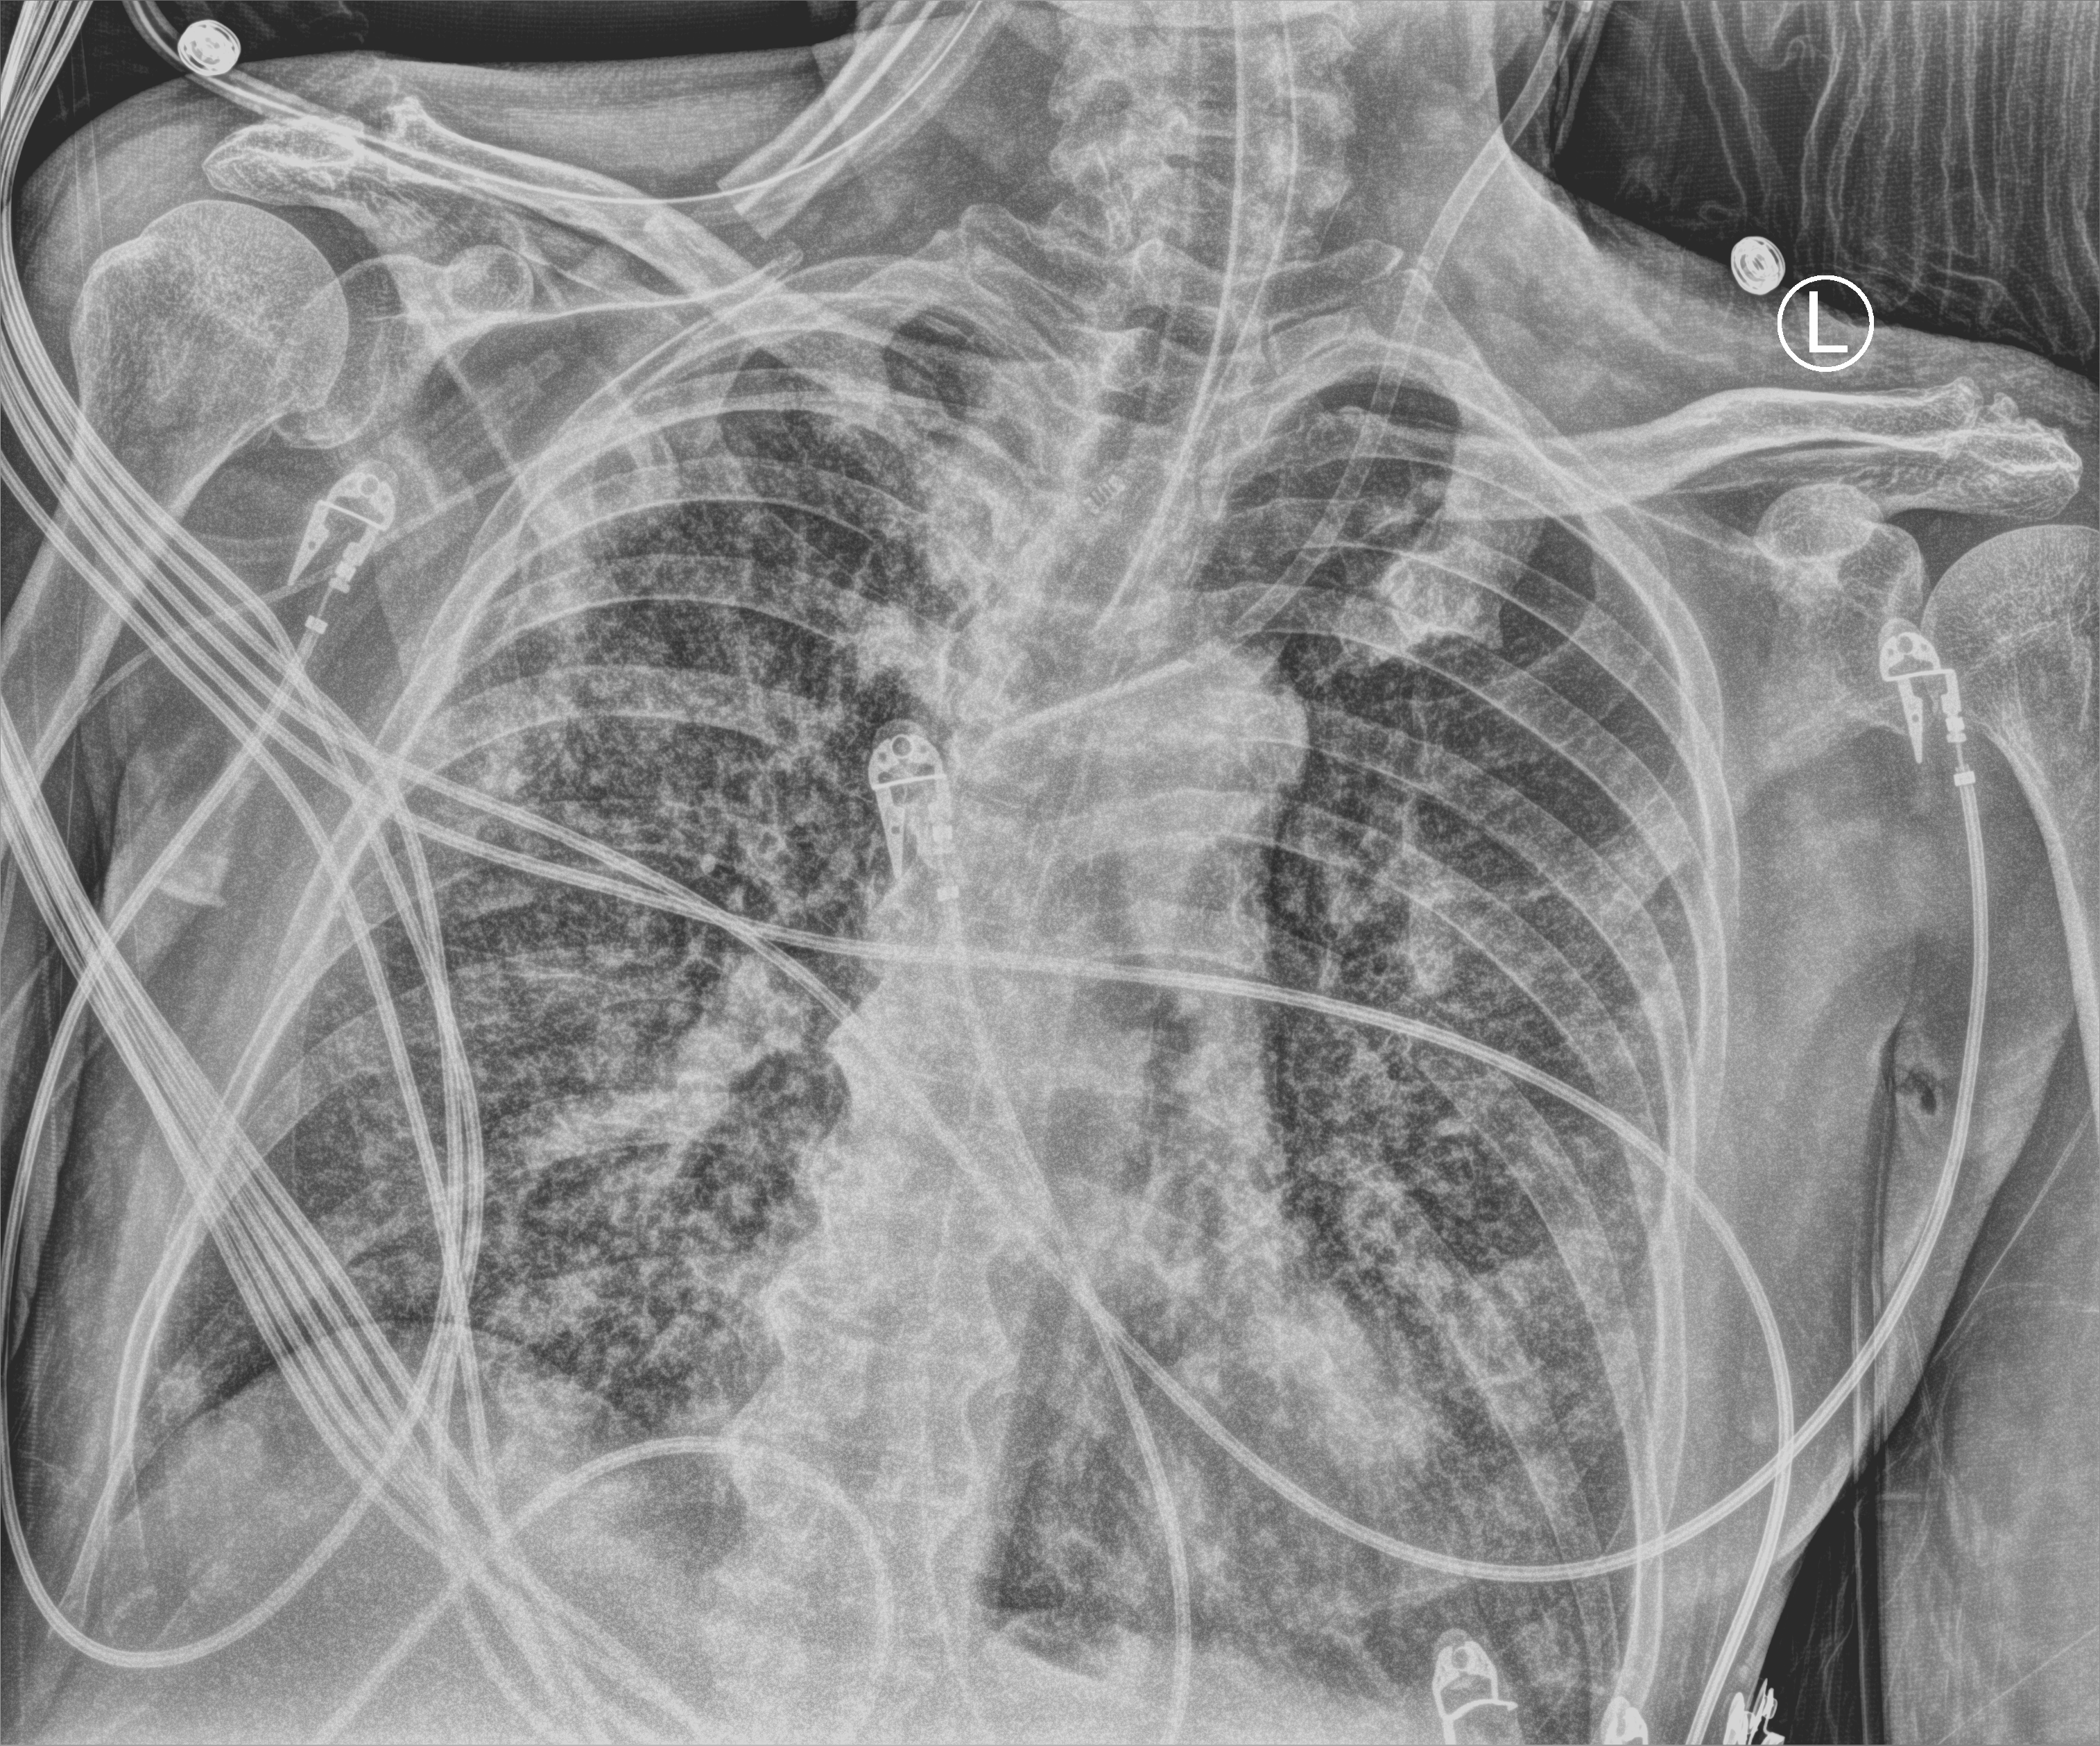
Portable chest radiograph; anteroposterior (AP) projection. Male patient hospitalised with COVID-19, age 60–74 years.
Hospital-stay facts (about this admission, not read from this image; timing relative to this image not recorded): hypertension (admission record): yes; diabetes (admission record): no.